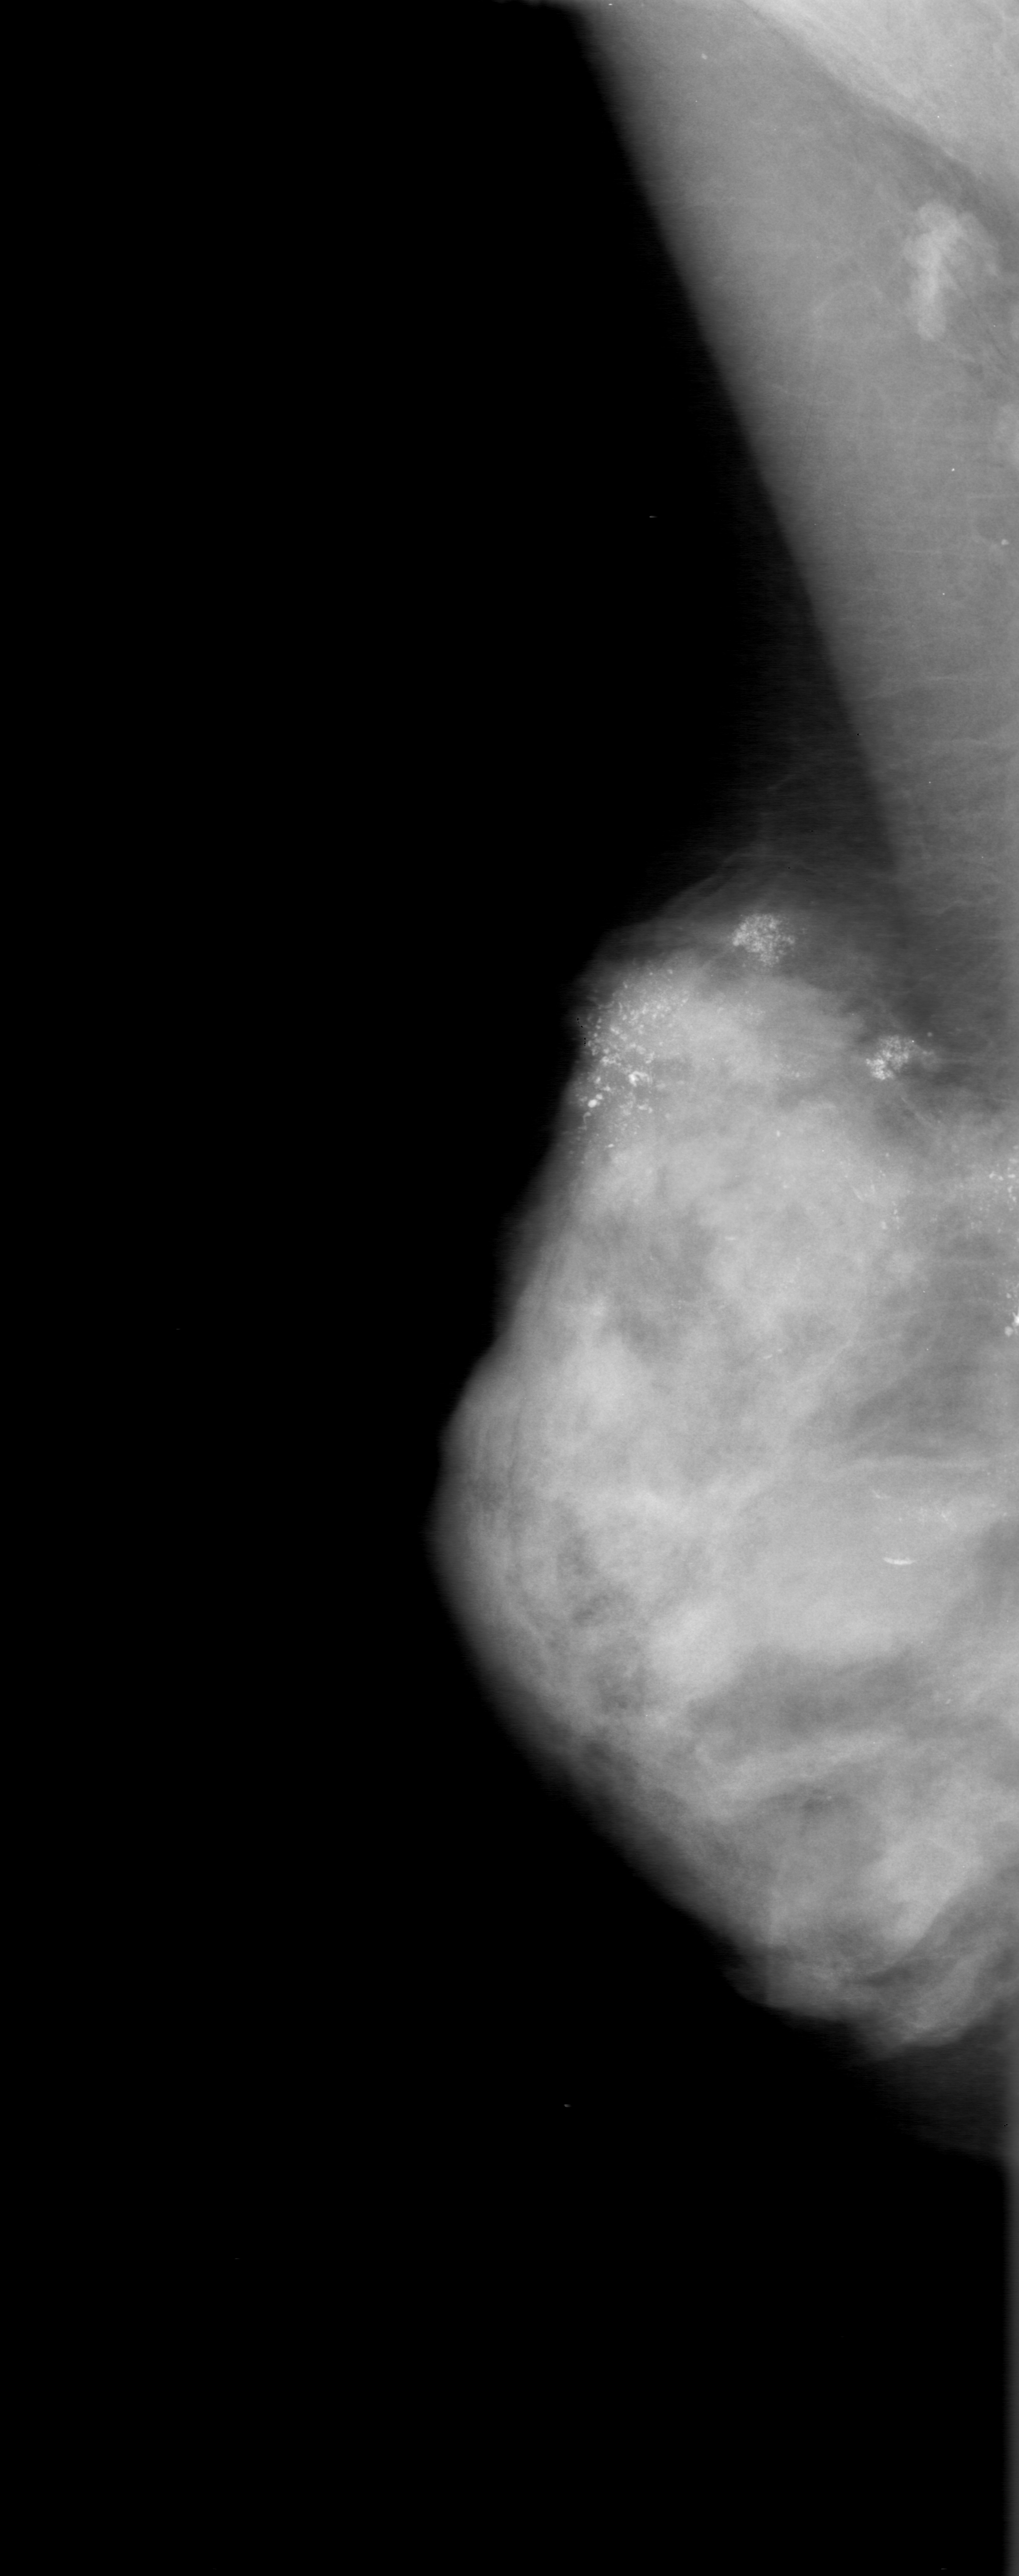
Mammogram (digitized film). Right breast. Mediolateral oblique (MLO) view. 1019 × 2576 image matrix.
Expert-marked regions of interest on this film, with their recorded descriptors:
- calcifications, morphology pleomorphic, distribution segmental; BI-RADS assessment category 5; subtlety rating 5 on a 1 (subtle) to 5 (obvious) scale; pathology result (as recorded, not read from the image): malignant: box from (x=487, y=818) to (x=1008, y=1616) px